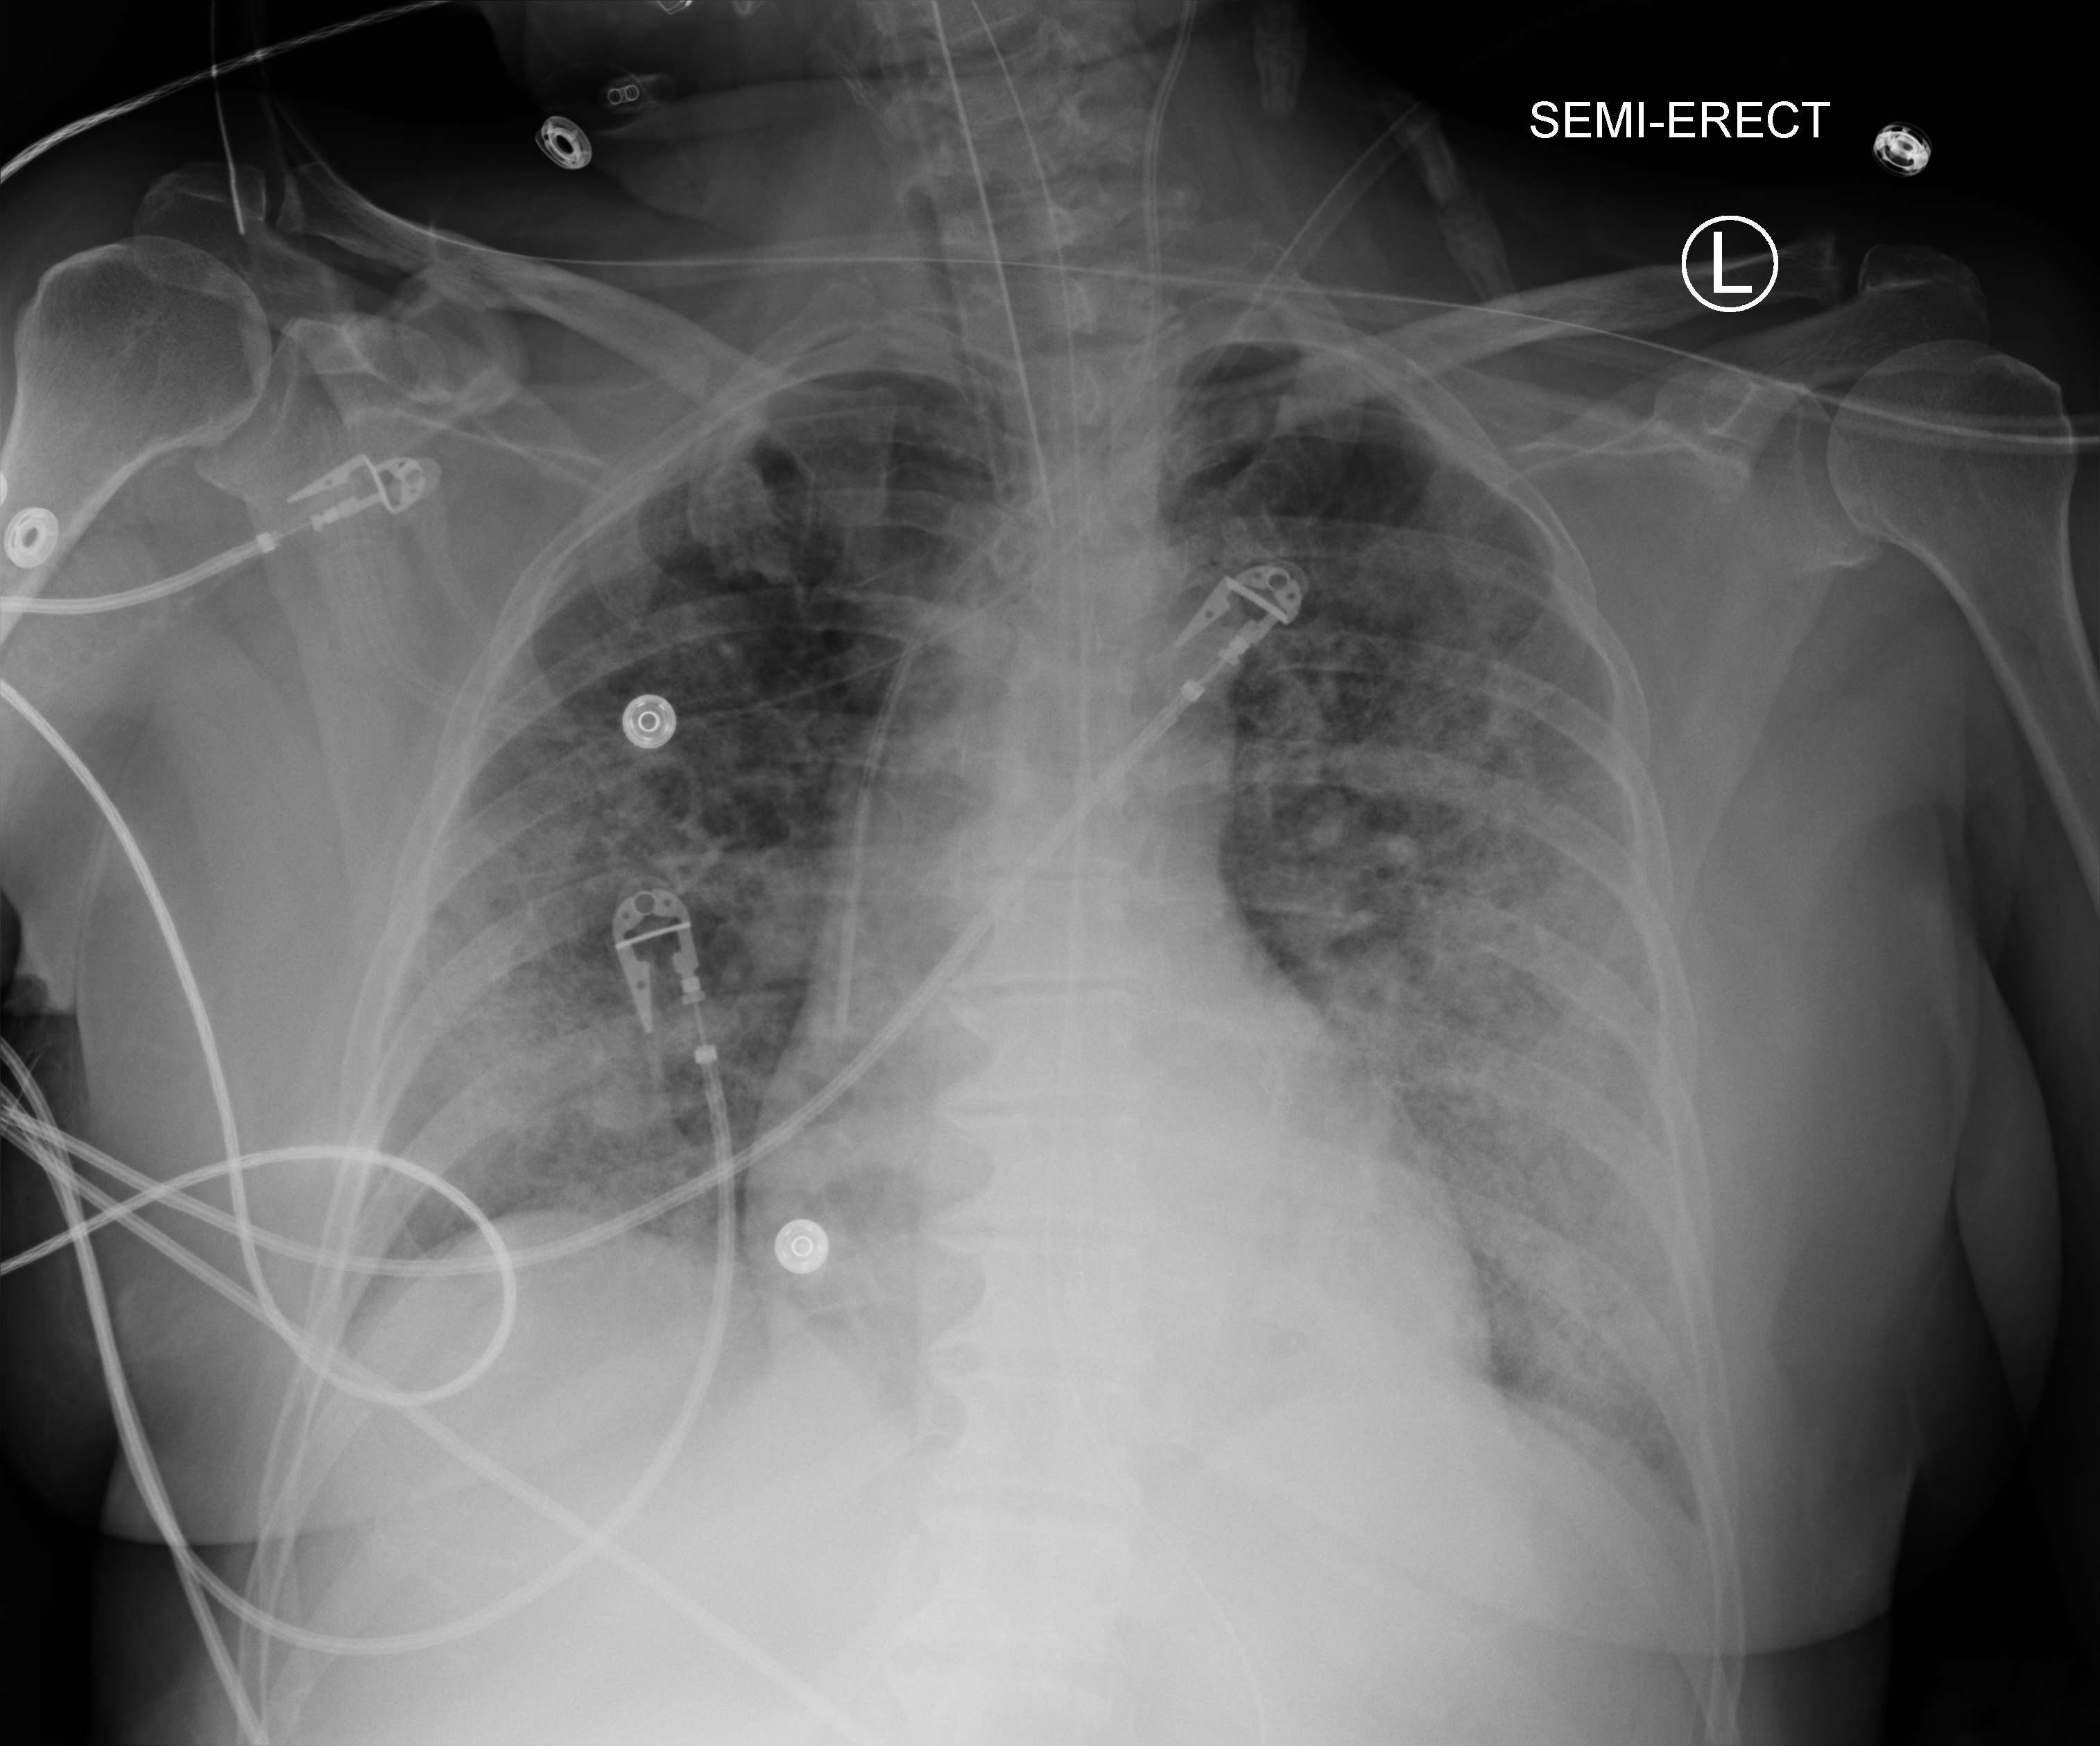
Chest X-ray (portable); anteroposterior (AP) projection. Patient hospitalised with COVID-19; female, aged 60–74 years.
Hospital-stay facts (about this admission, not read from this image; timing relative to this image not recorded): length of hospital stay: 24 days.